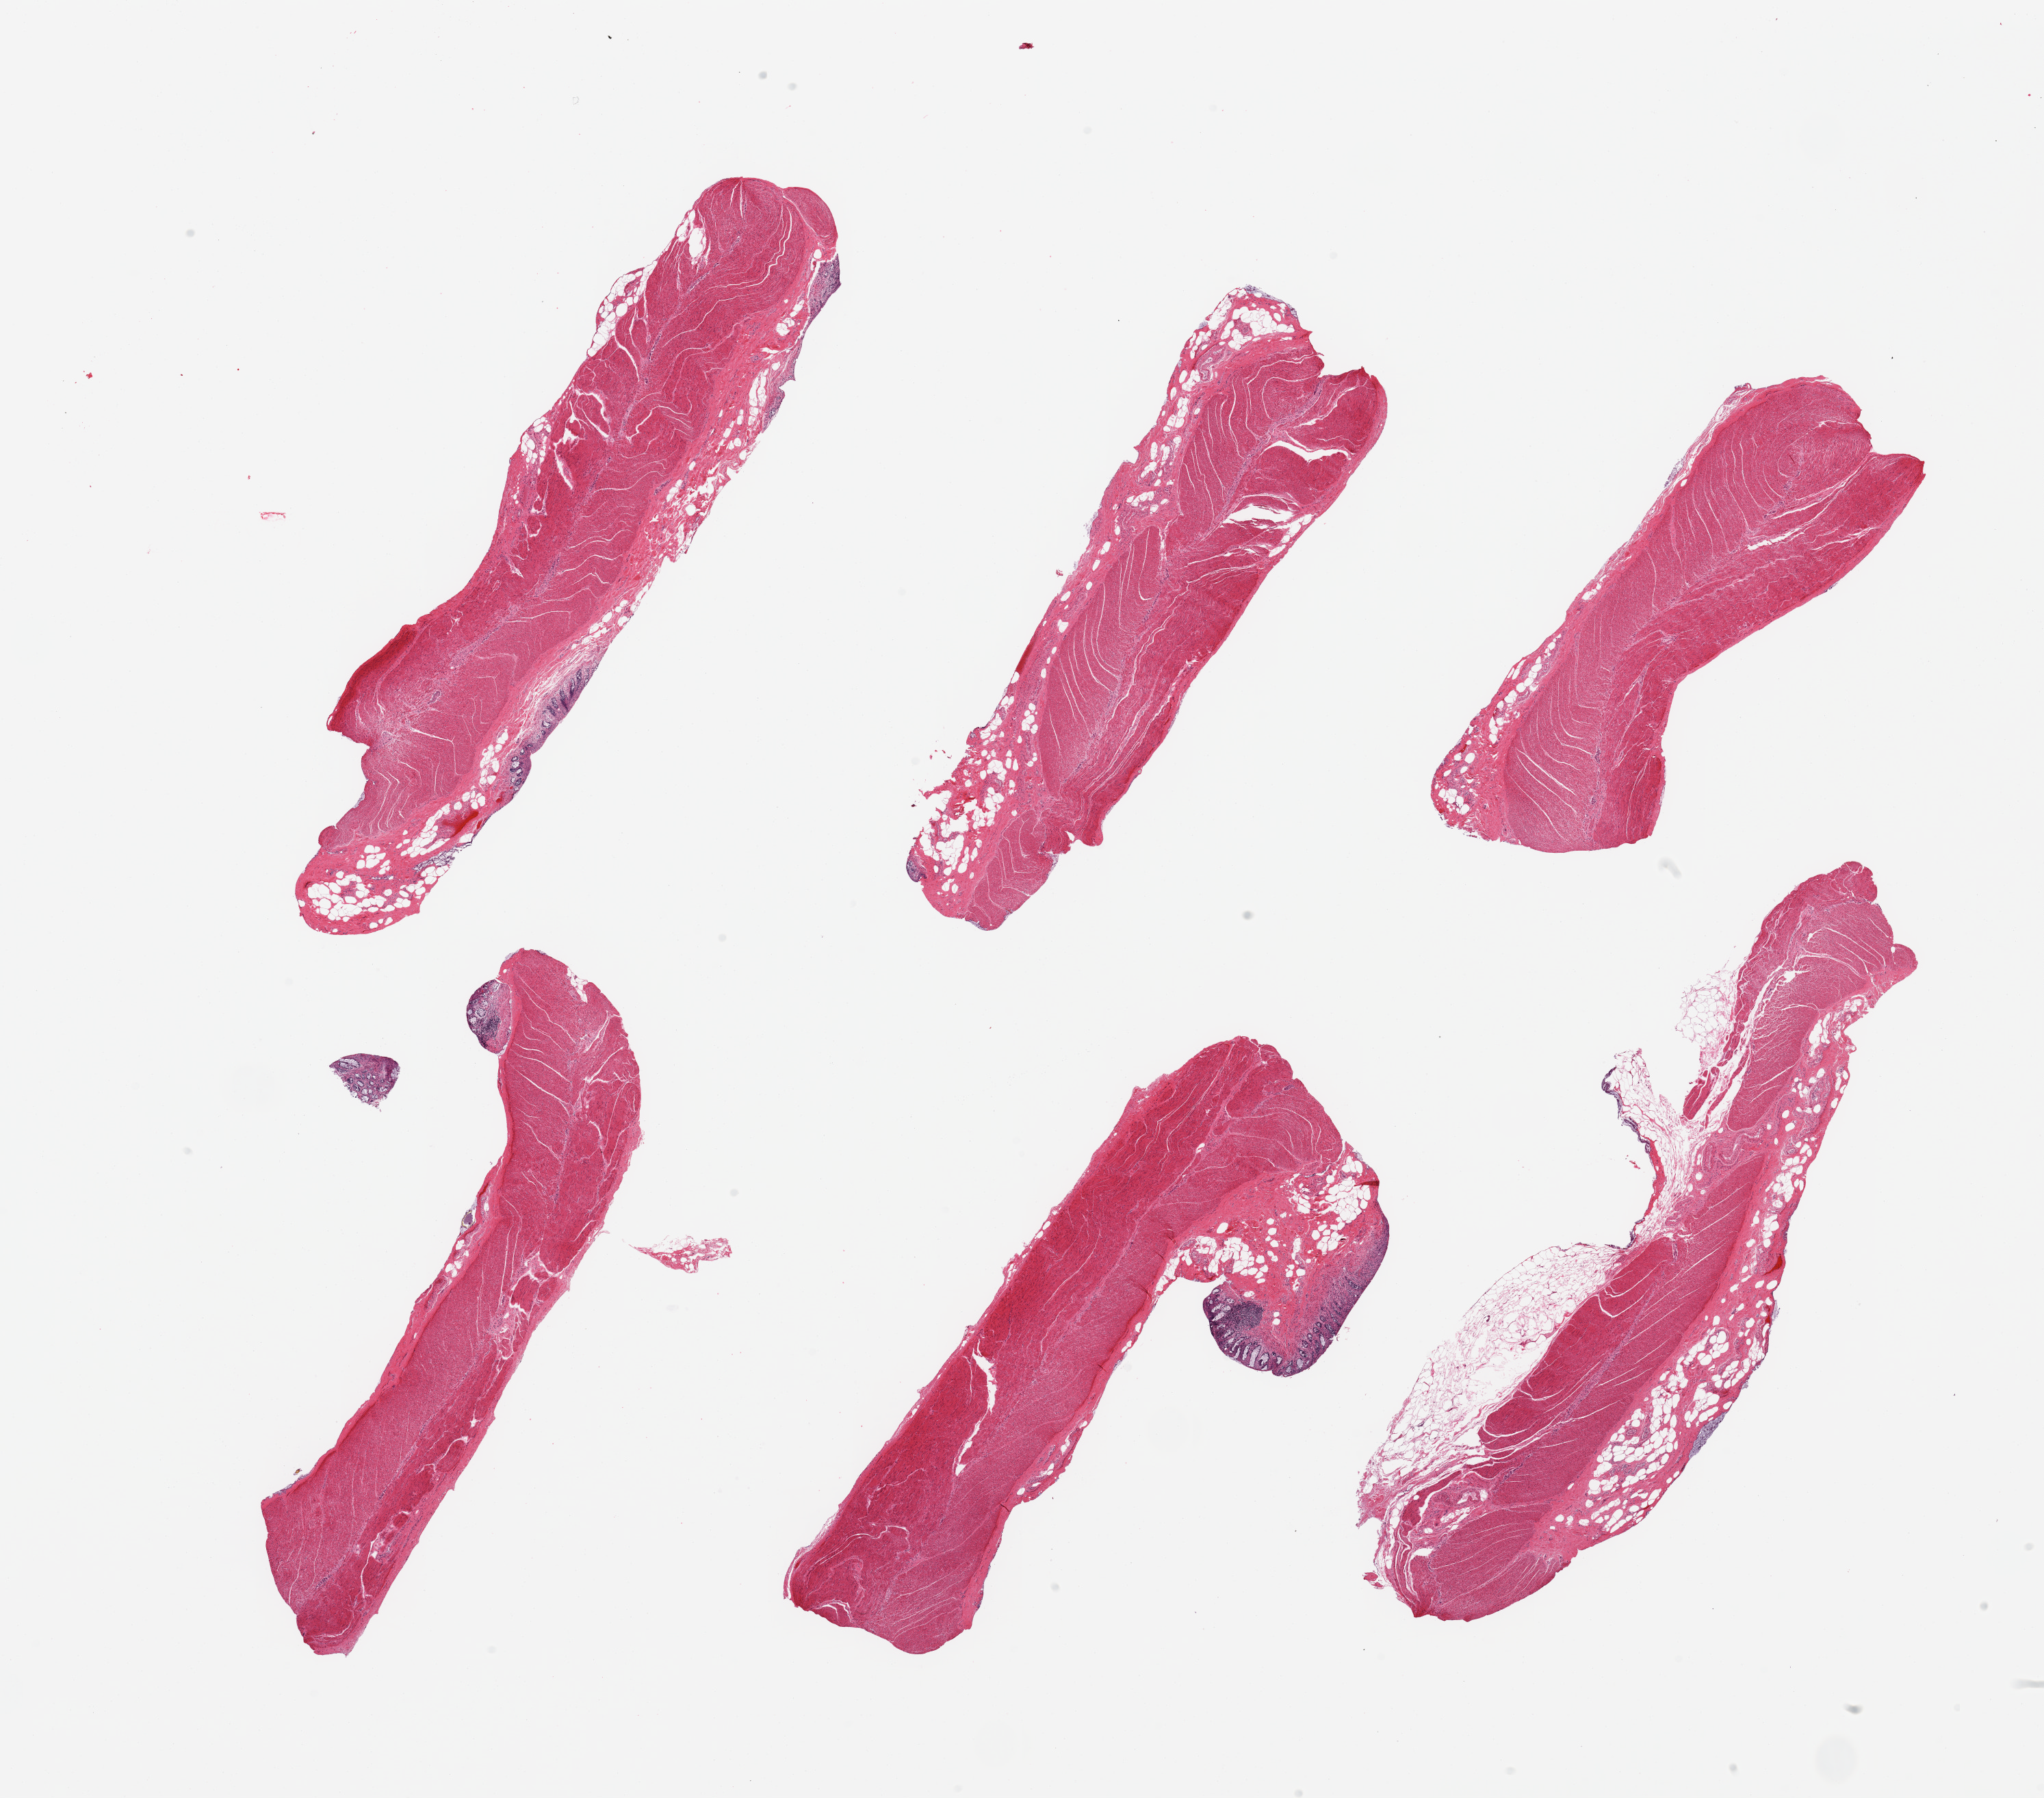
Haematoxylin and eosin whole-slide image — low-resolution overview of the scanned area, about 23.6 x 20.8 mm; PAXgene-fixed paraffin-embedded (PFPE) section; target tissue: sigmoid colon; donor tissue sample.
• review note (as recorded): 6 pieces, confirmed target muscularis; trace contaminant autolyzed mucosa